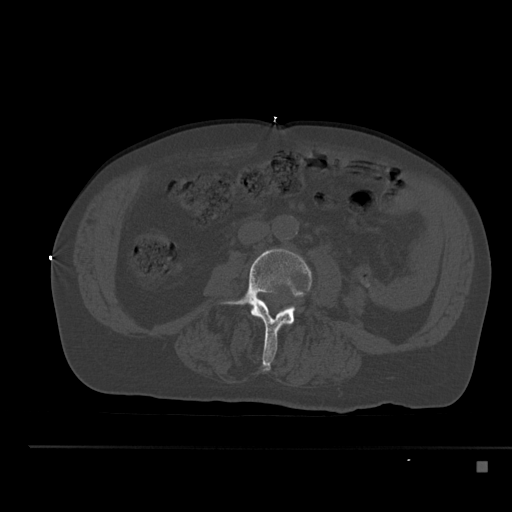
CT including the spine, one axial slice; position 161 of 517 along the scan axis; reconstruction kernel Br40s; bone window (W 1800 / L 400 HU); 1.5 mm slice thickness; 512 × 512 image matrix. Male patient, age 70 years. From the clinical record (not read from this slice): primary cancer: renal; vertebrae with lytic lesions (as recorded): T4, T6, T10, T12, L3, L4, L5.
Structures marked on this image (semi-automatic segmentation, software-assisted and operator-edited):
- L3 vertebra: box from (x=221, y=249) to (x=312, y=370) px